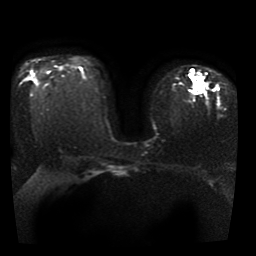
Breast MRI, one axial slice. Slice 26 of 41 in the series (ordered by position). Diffusion-weighted series; image 2 of 4 stored at this slice position (different b-values; order by instance number). 1.5 T. 5 mm slice thickness. 256 × 256 image matrix, field of view 330 × 330 mm. Female patient.
Structures marked on this image (manually delineated by an expert):
- tumour on diffusion-weighted imaging: bounding box <187,69,207,93> (left, top, right, bottom; pixels)